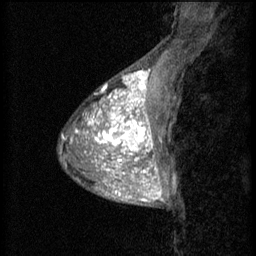
Breast MRI (dynamic contrast-enhanced), one sagittal slice; slice 17 of 60 in the series (ordered by position); 3 images stored at this slice position (order not interpretable as contrast timing); 1.5 T; TE 4.2 ms, TR 8.2 ms; 2 mm slice thickness; 256 × 256 image matrix. Female patient, age 38 years.
Outlined on this slice (semi-automatic segmentation, software-assisted and operator-edited):
- analysis volume of interest (the breast-tissue region the enhancement analysis was run in; not a lesion): bounding box <95,106,157,171> (left, top, right, bottom; pixels)
- tumour enhancement mask (voxels above the 70 % enhancement threshold inside the analysis volume of interest): <95,106,157,171>